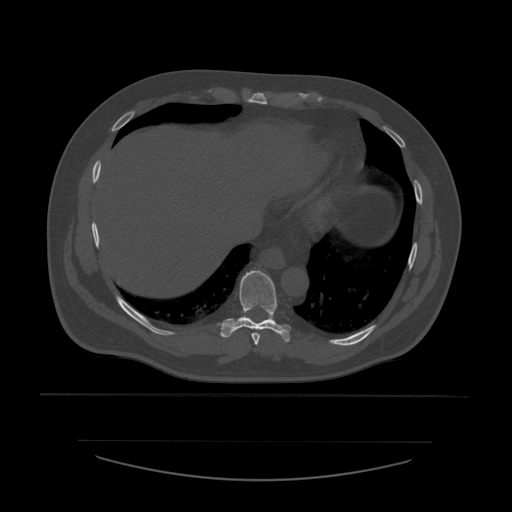
CT including the spine, one axial slice; position 319 of 532 along the scan axis; 120 kVp; bone window (W 1800 / L 400 HU); 512 × 512 image matrix, field of view 441 × 441 mm. Patient age 44 years. From the clinical record (not read from this slice): primary cancer: soft tissue sarcoma.
Annotated regions visible in this slice (semi-automatic segmentation, software-assisted and operator-edited):
- T8 vertebra: box from (x=252, y=333) to (x=260, y=346) px
- T9 vertebra: (x=218, y=271)–(x=291, y=342)